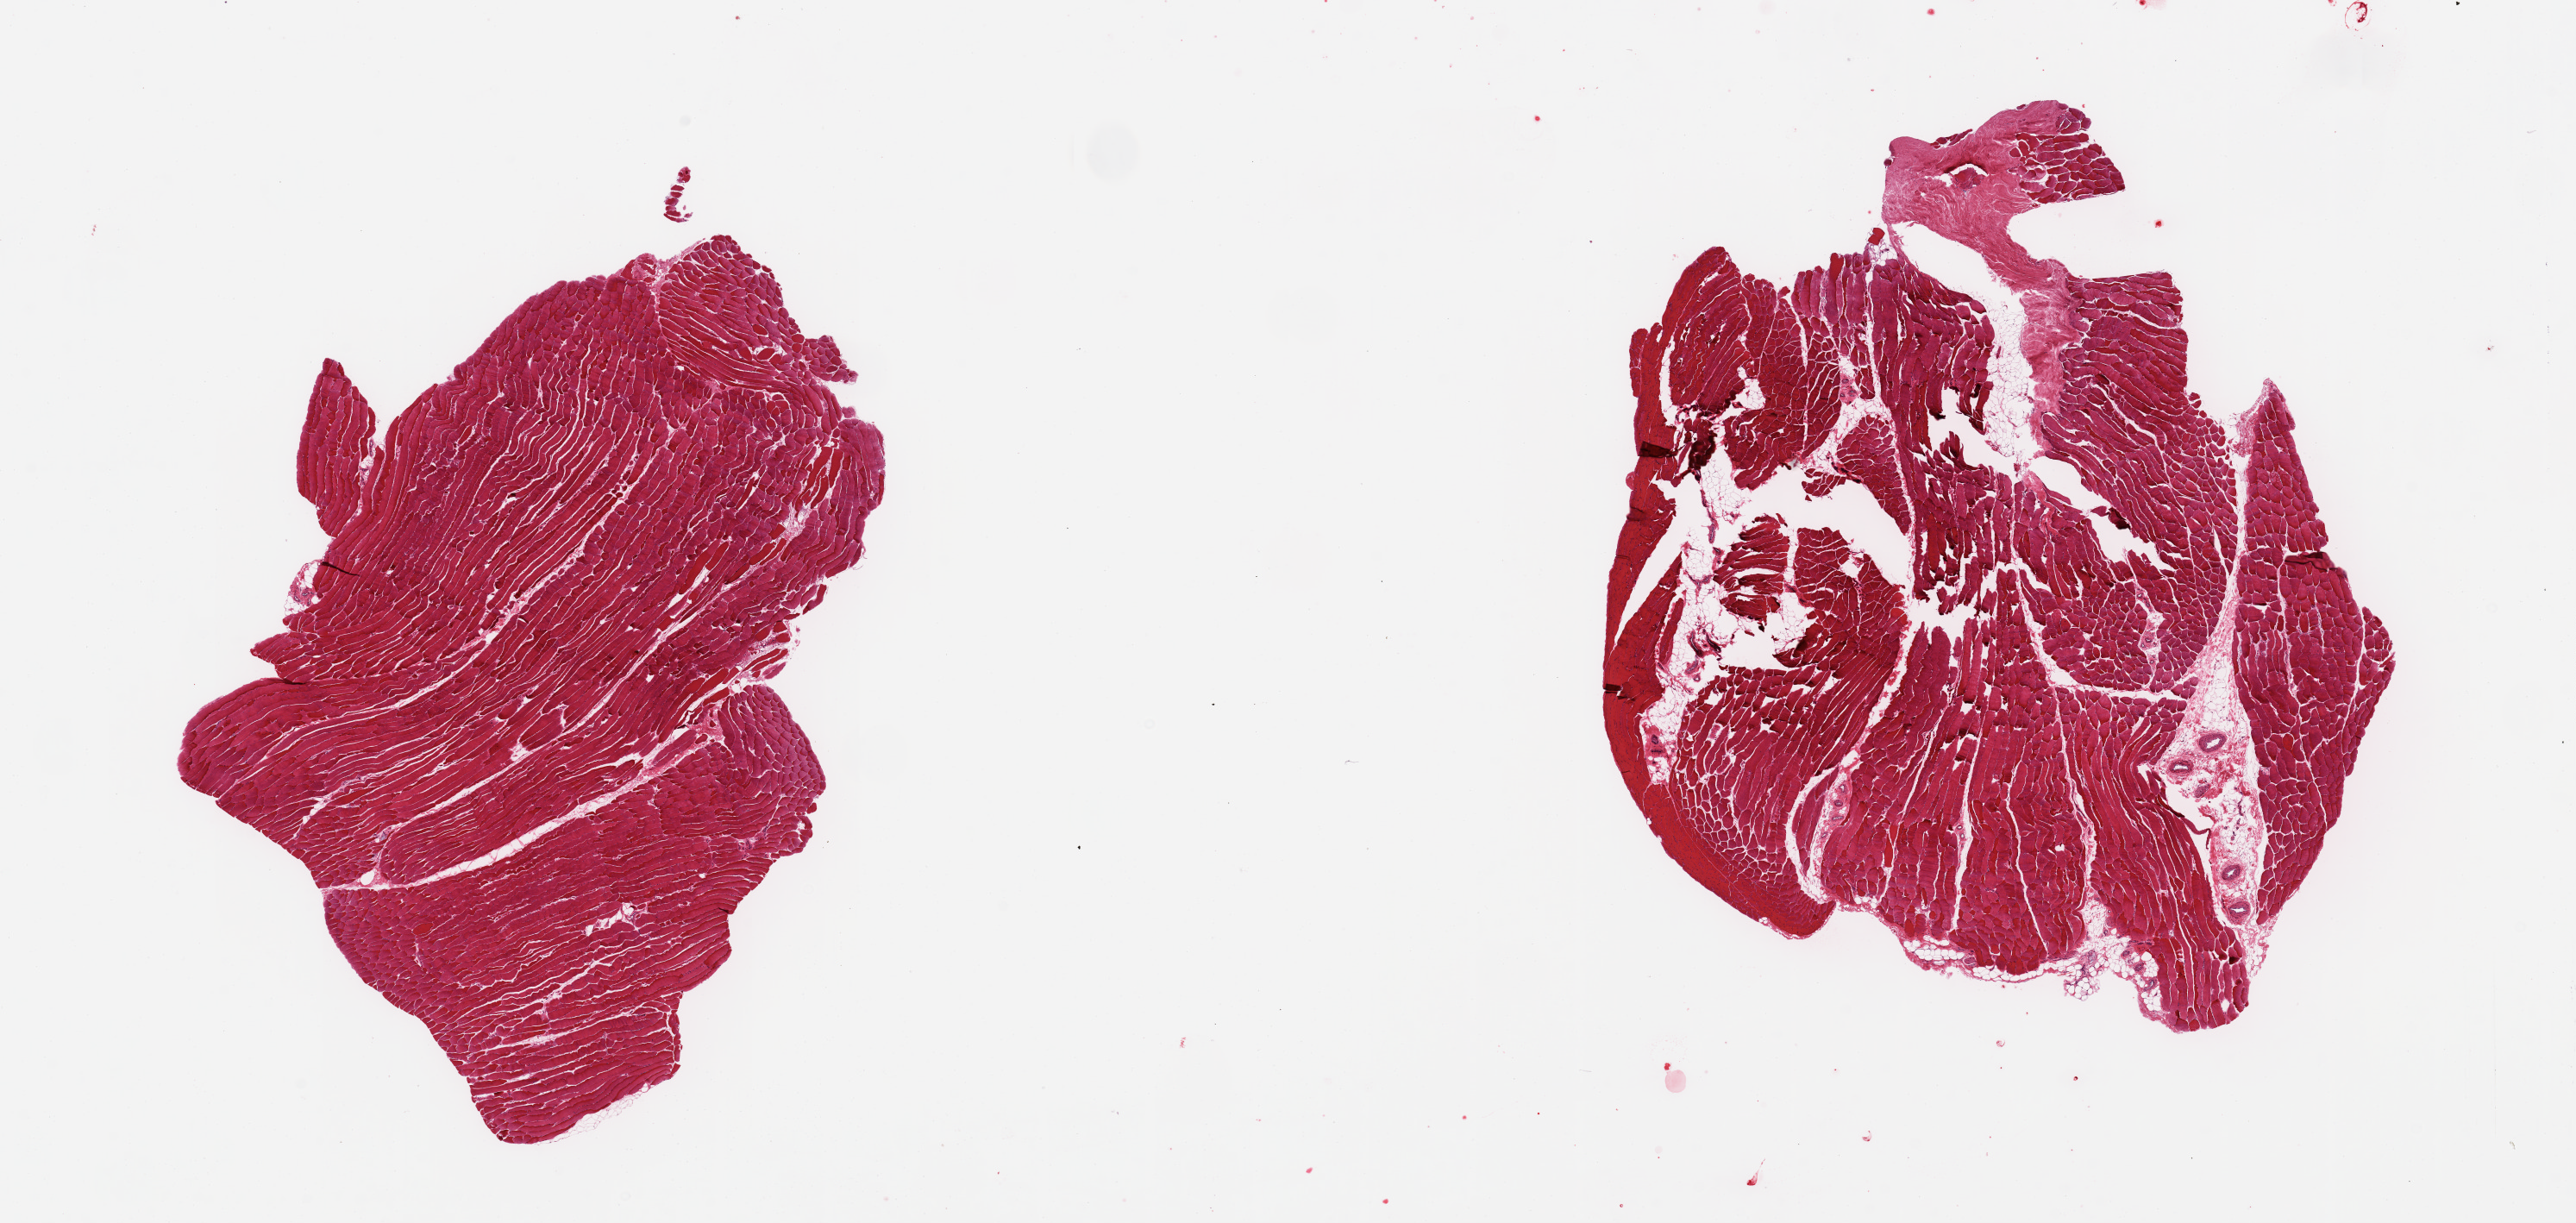
Digitized hematoxylin and eosin (H&E)-stained section, brightfield, a low-resolution overview of the entire scanned area, about 23.6 x 11.2 mm; PAXgene-fixed, paraffin-embedded tissue; section of skeletal muscle (target tissue); donor tissue sample. Donor sex: female.
Review note (as recorded): 2 pieces; mild to moderat autolysis; generalized atrophy; one contains ~15% internal/external fat, fibromuscular component and empty spaces.